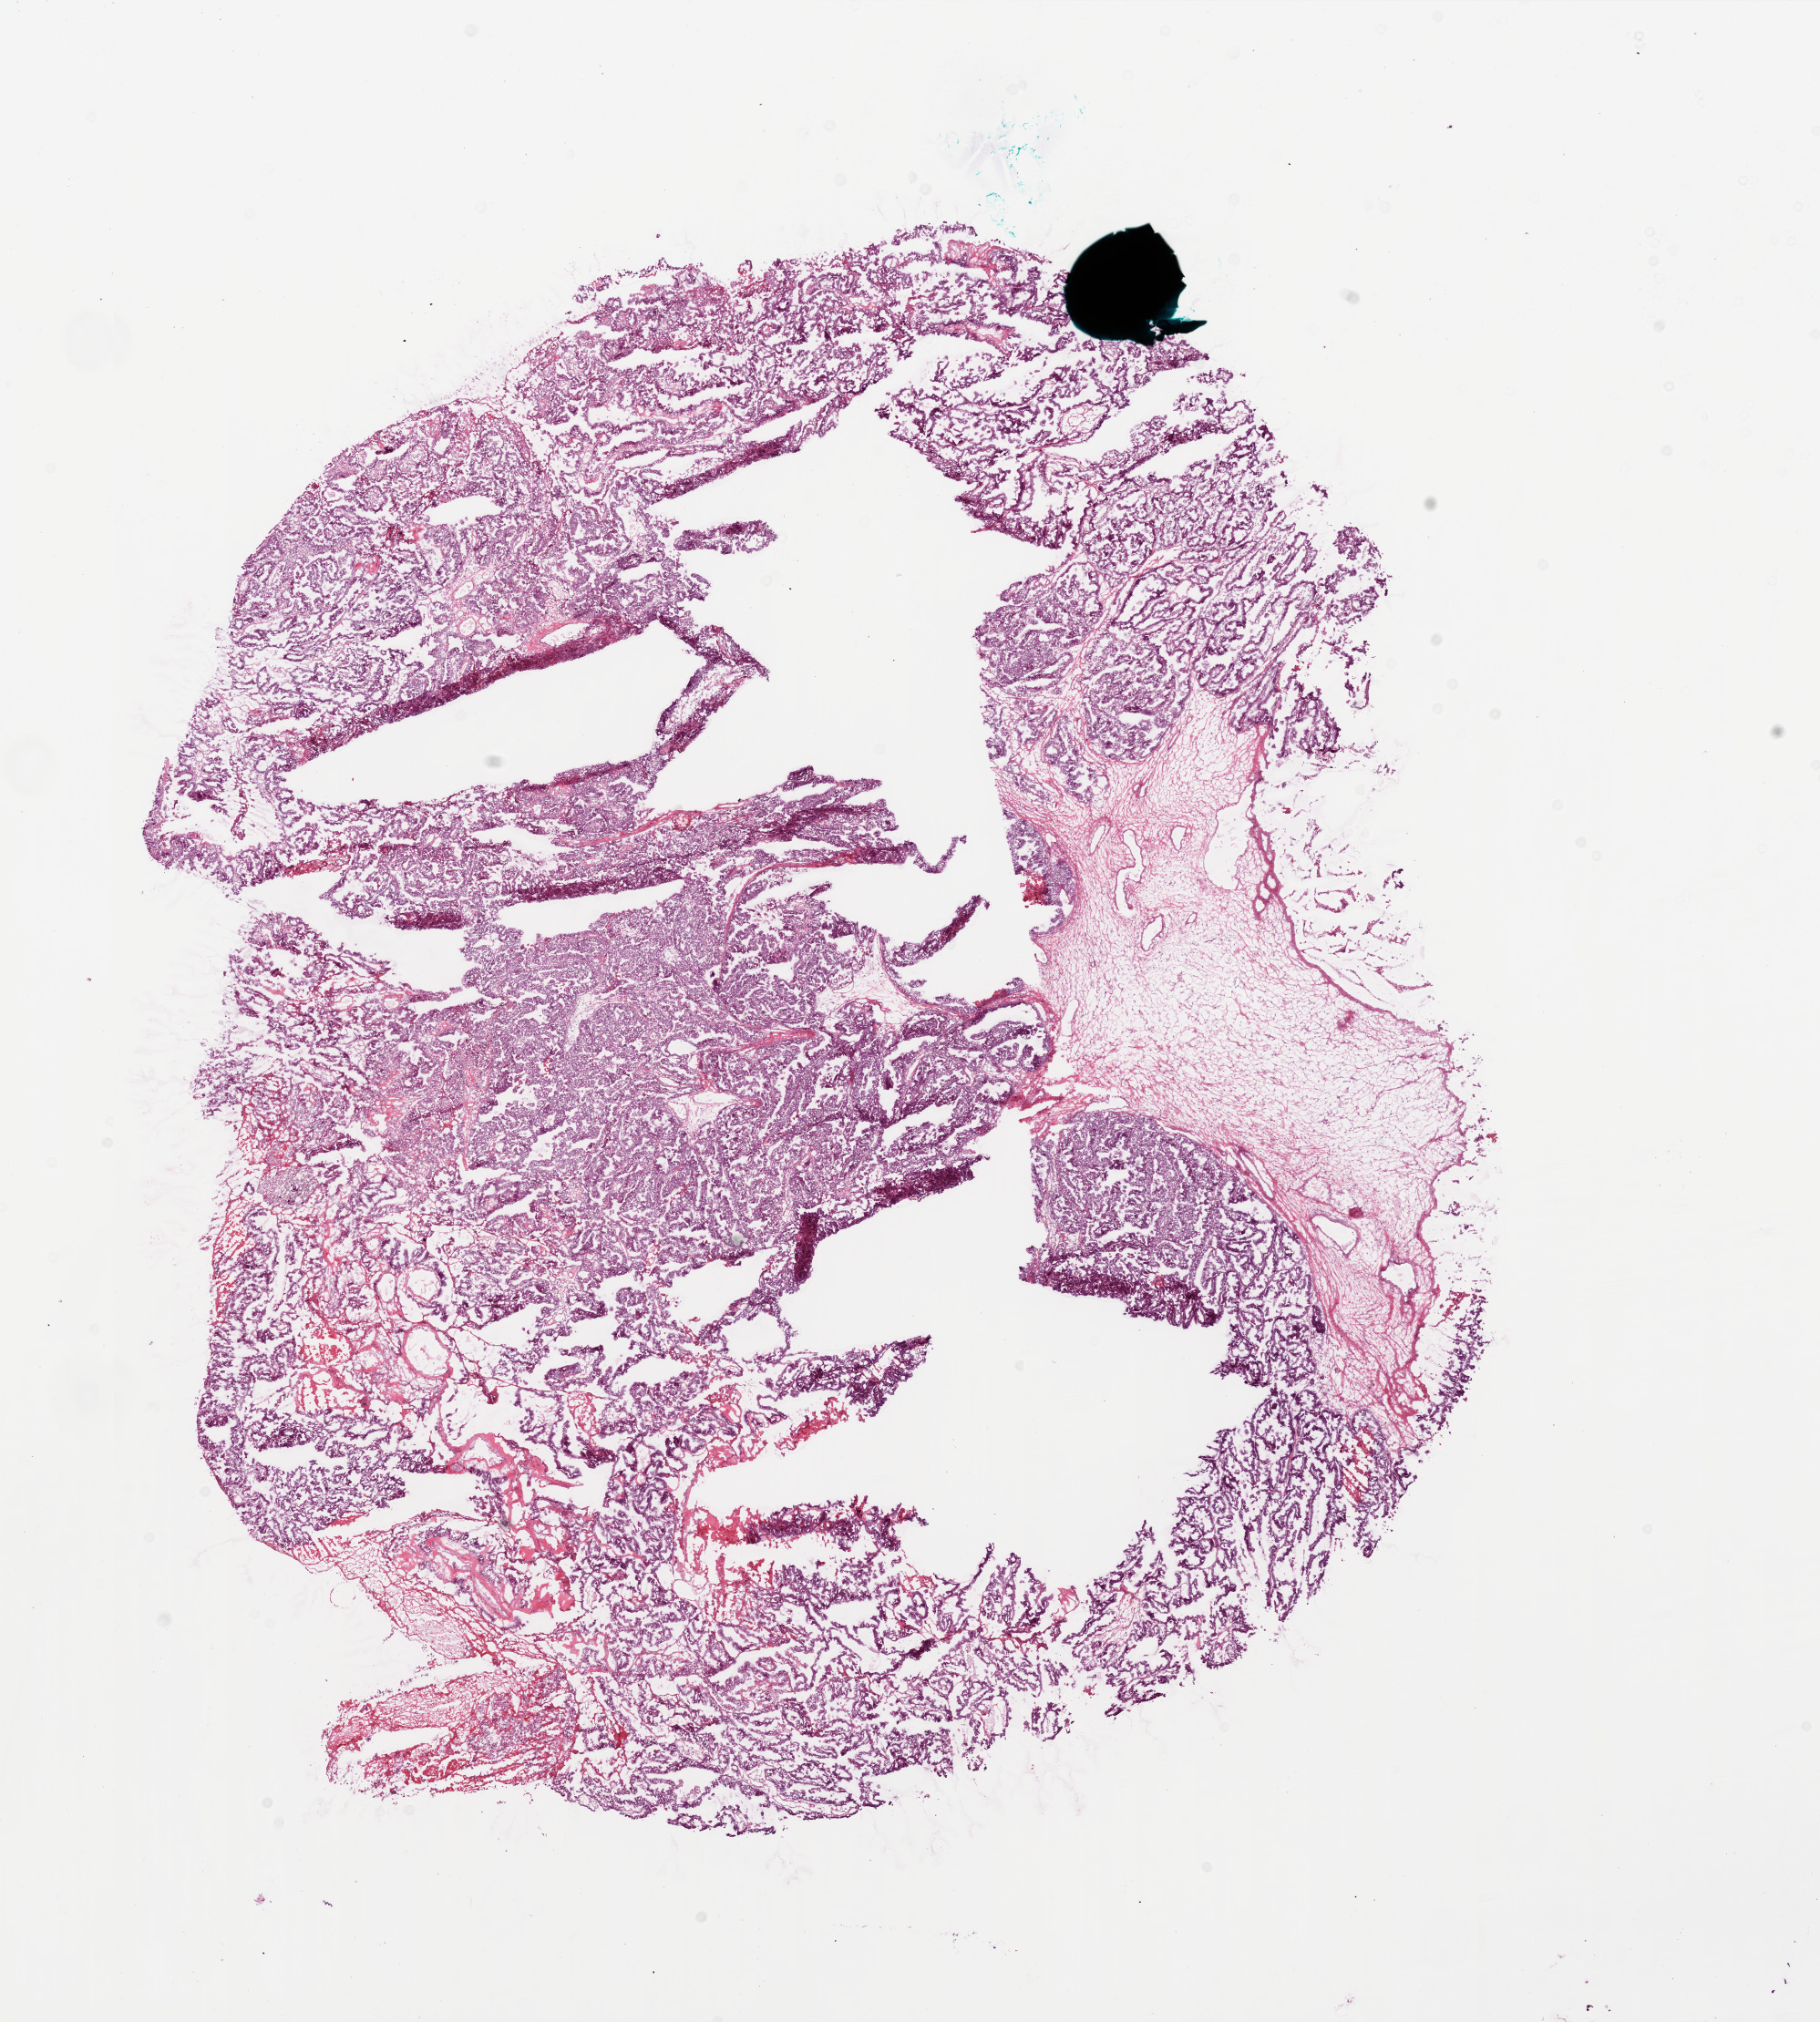
Whole-slide histology image, H&E-stained, a low-resolution overview of the entire scanned area, about 16.0 x 17.8 mm, frozen section from the bottom of the tissue portion, sample: primary tumour, ovary. Female patient; age at initial diagnosis 74 years. Histologic grade: G3 (poorly differentiated). Slide review estimates, as recorded: tumour cells 70%, tumour nuclei 85%, normal cells 0%, stromal cells 25%, necrosis 5%.
Laterality: right. Pathologic diagnosis: Serous cystadenocarcinoma, NOS. FIGO stage: IIIC.